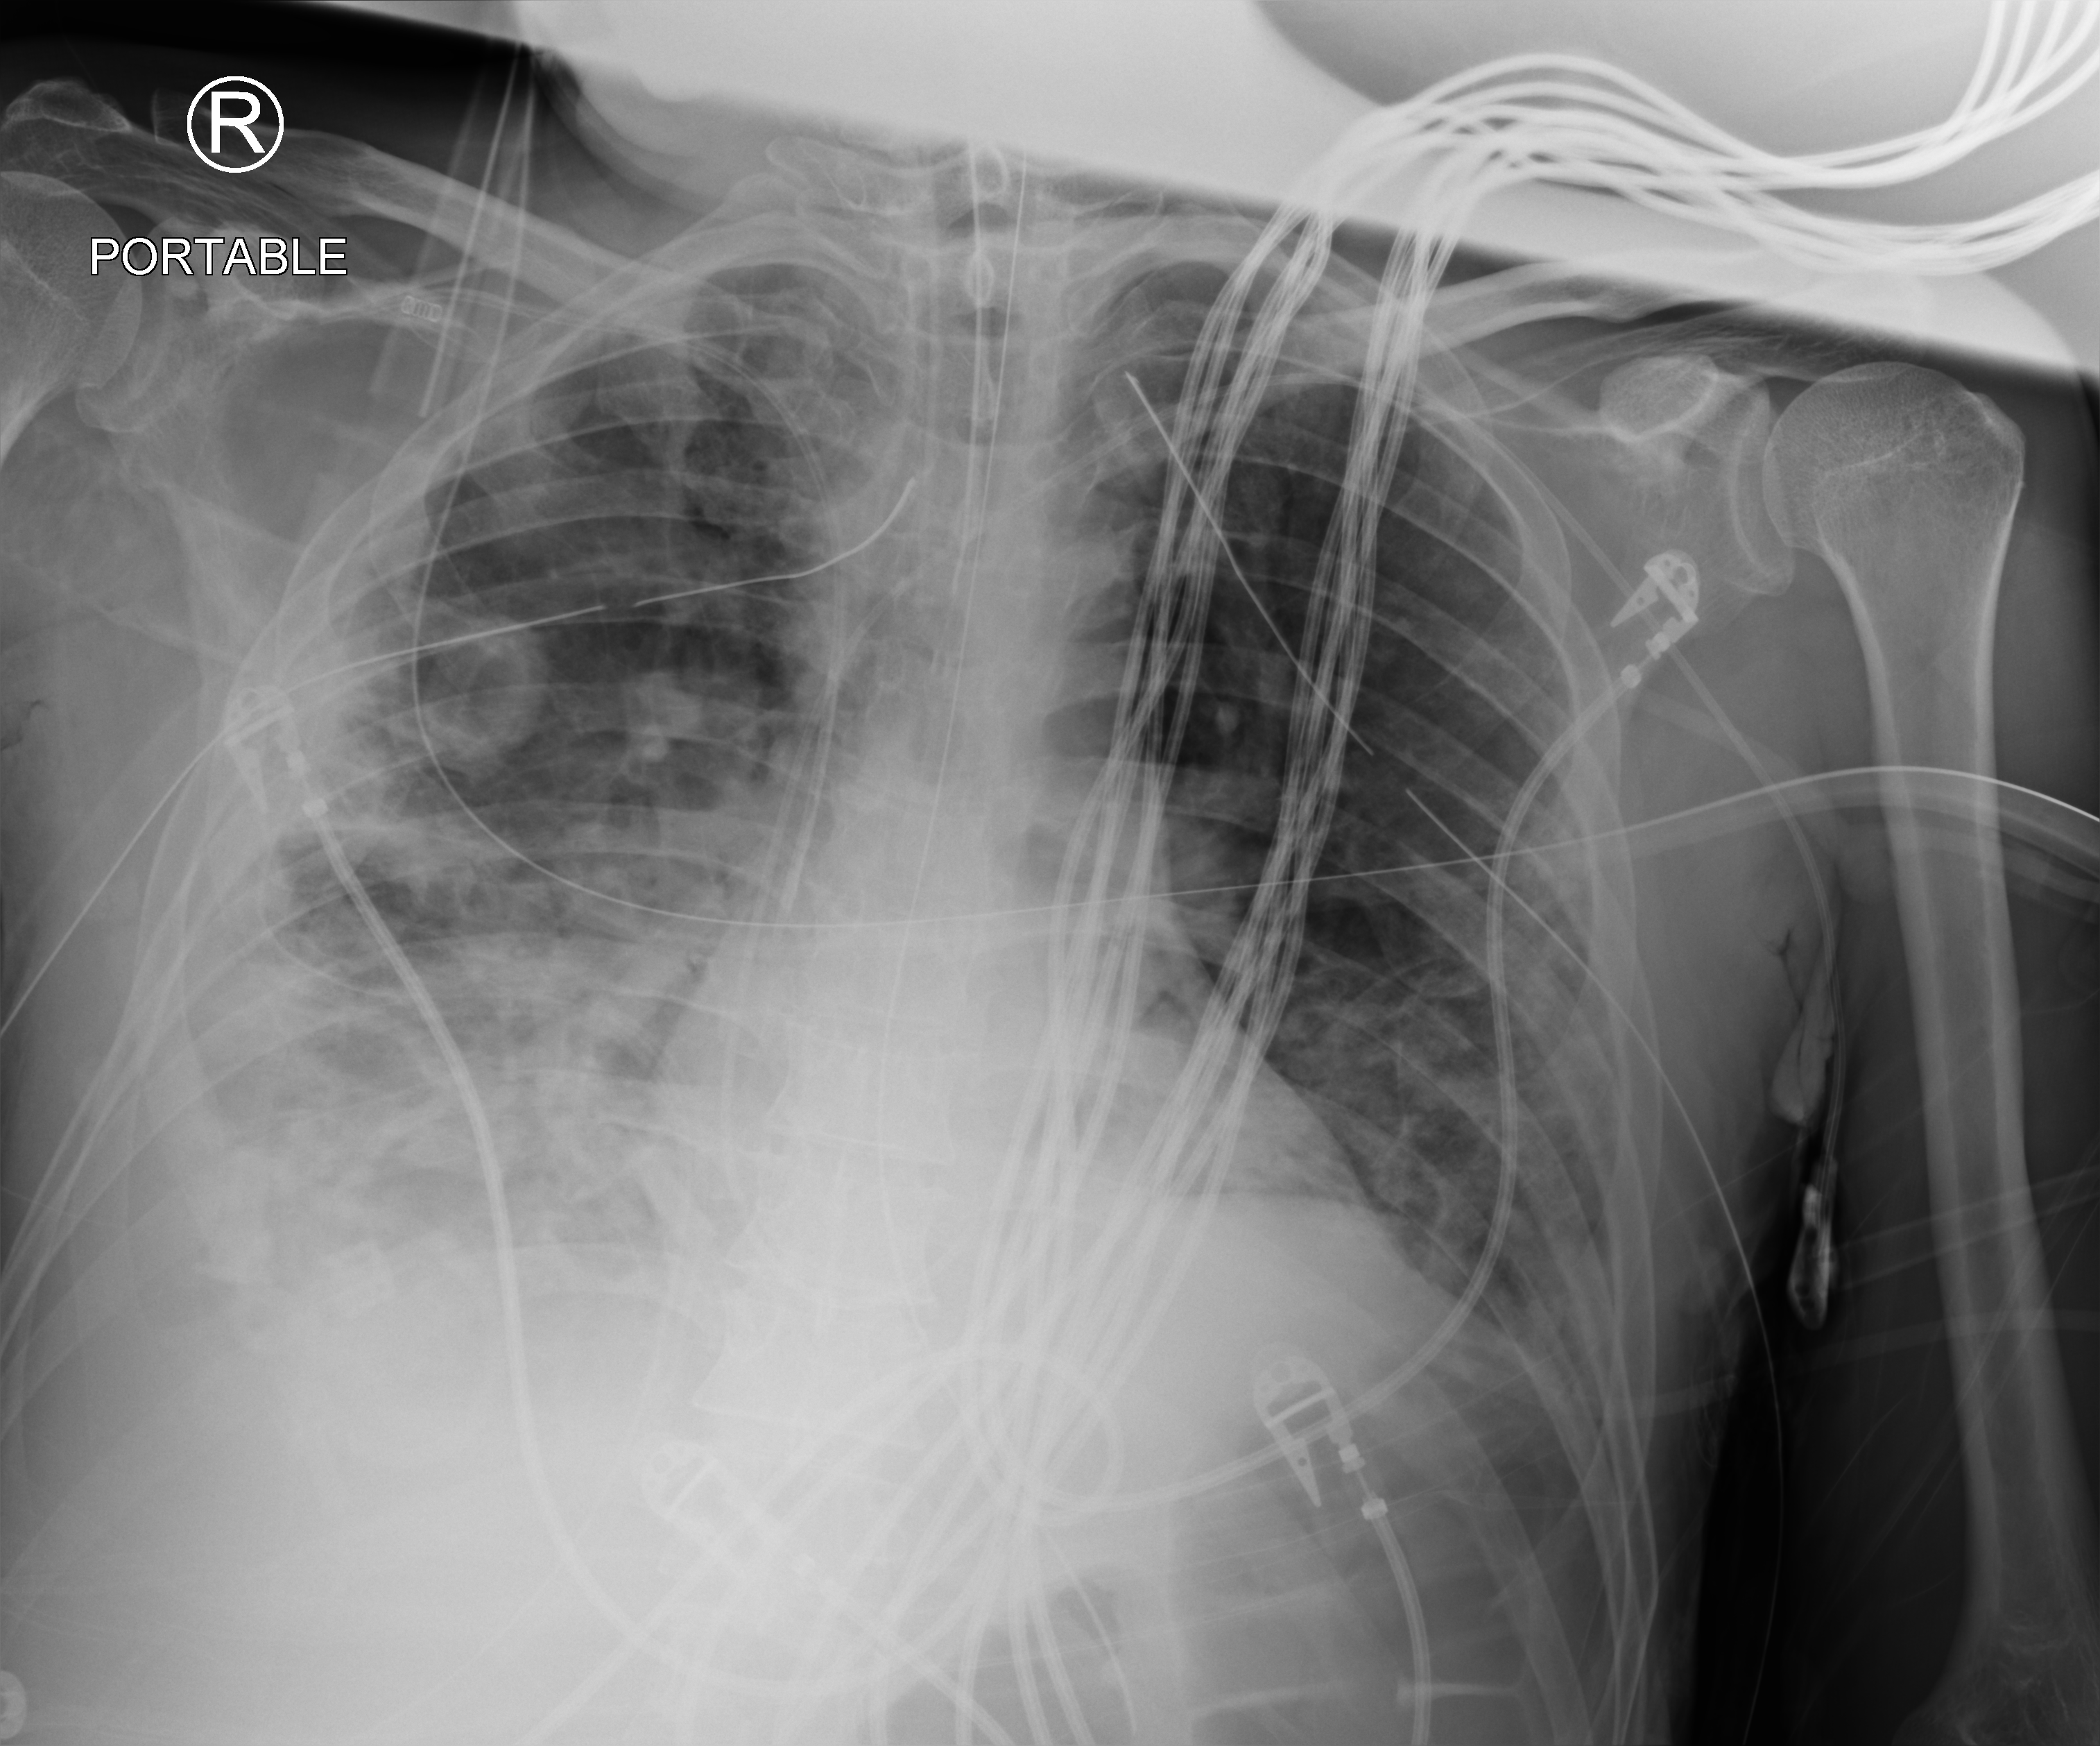
Portable chest radiograph. Male patient hospitalised with COVID-19, age 18–59 years.
From the hospital-stay record, not from the radiograph (when in the stay this image was taken is not recorded):
- admitted to intensive care during this hospital stay: yes
- smoking status (admission record): never